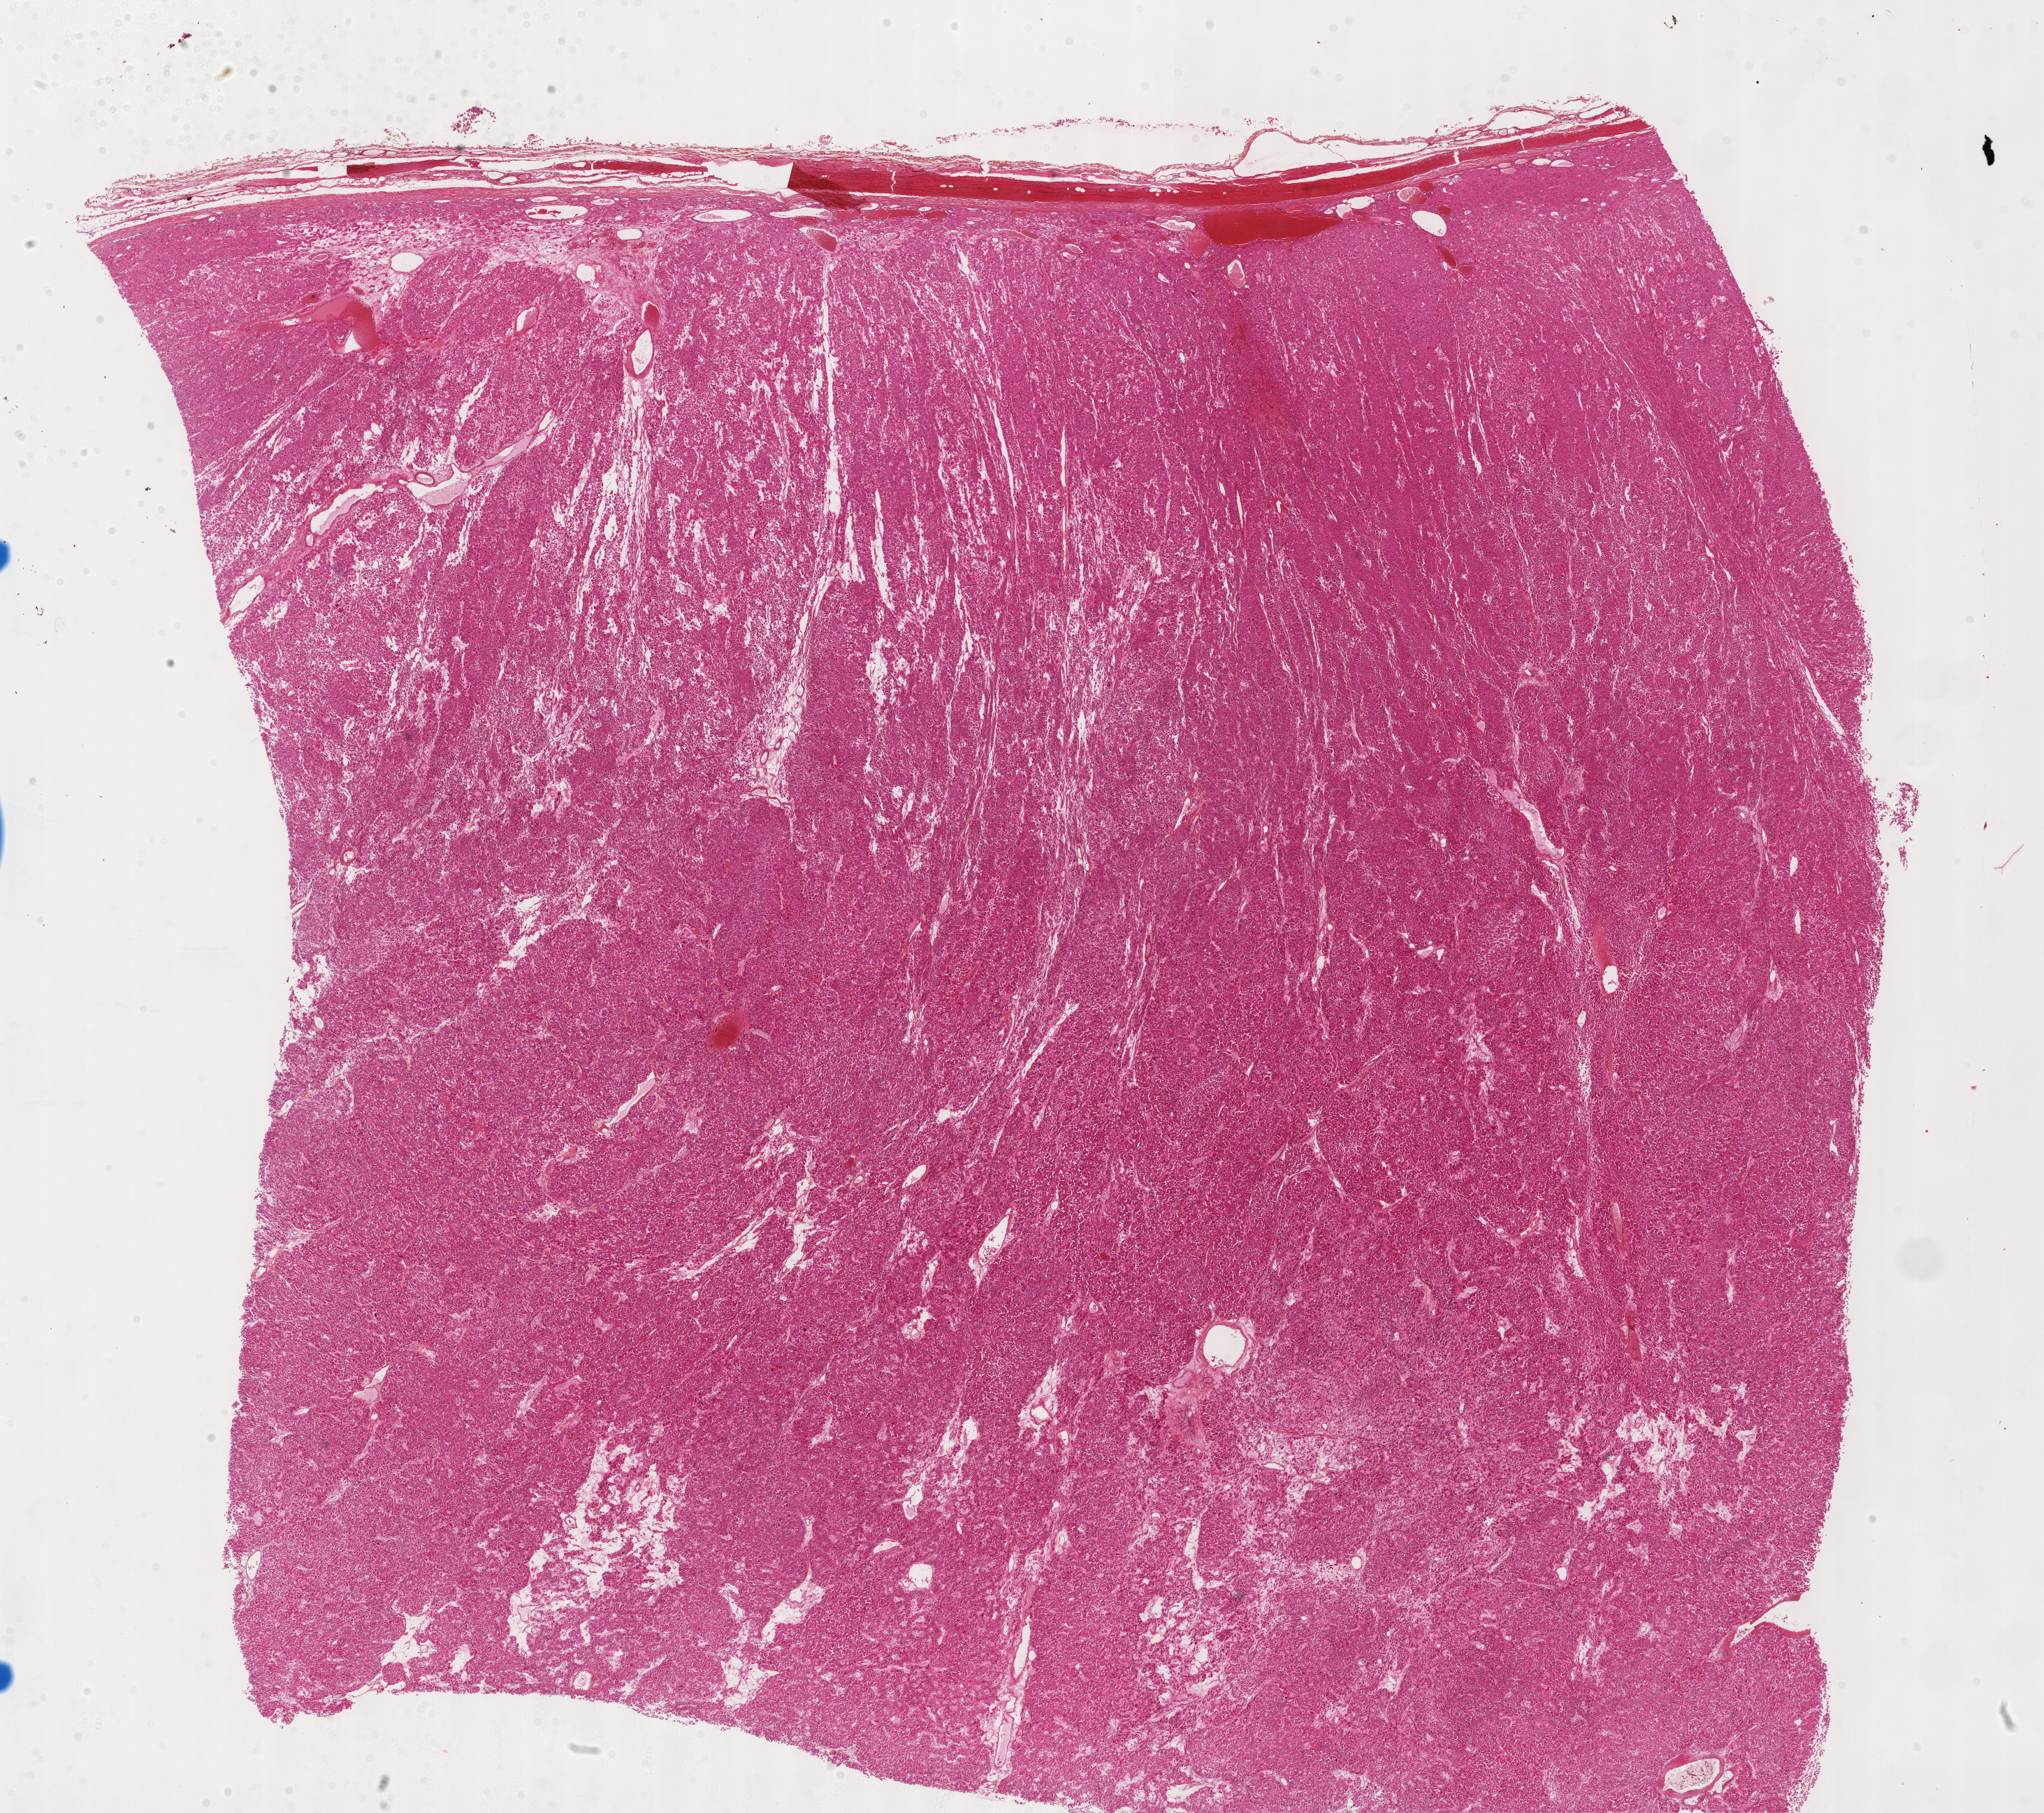
Digitized Hematoxylin and eosin (H&E) stained tissue section (whole slide) — low-resolution overview of the scanned area, about 23.6 x 21.0 mm (from a 40x scan), formalin-fixed paraffin-embedded (FFPE) diagnostic section, sample: primary tumour, adrenal cortex. Male, age 57 years at initial diagnosis.
Diagnosis: Adrenal cortical carcinoma.